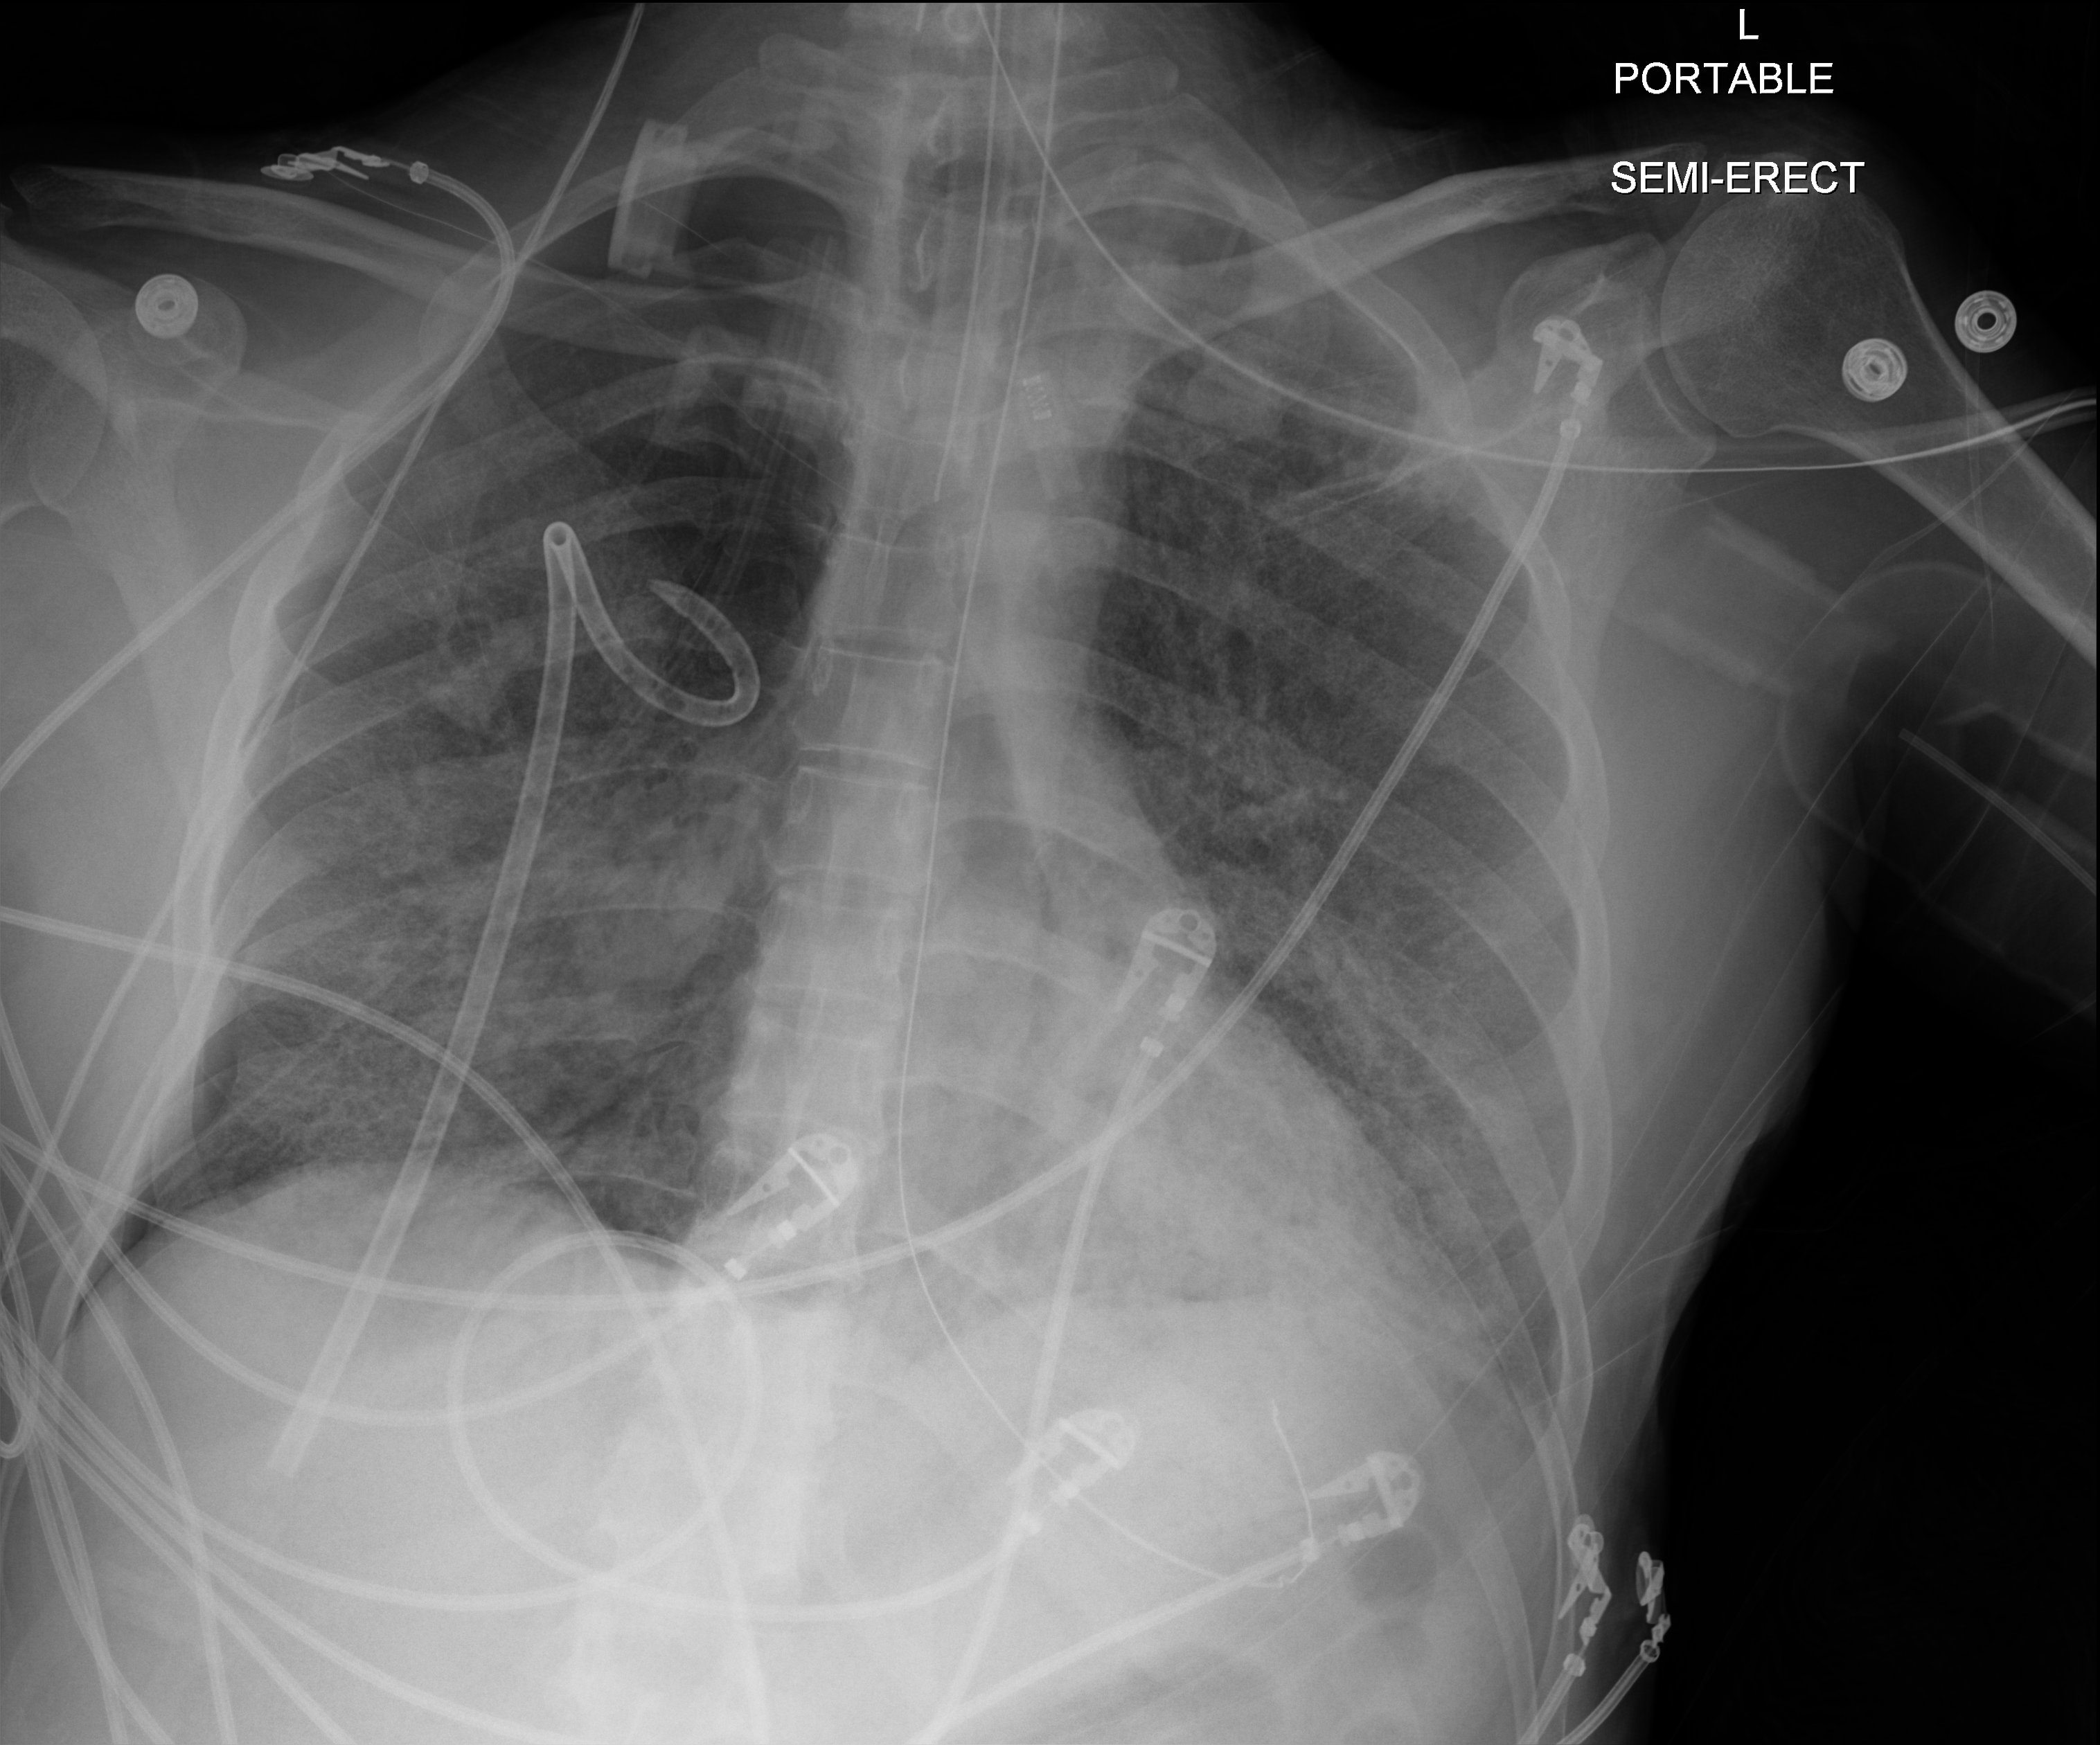
Chest radiograph, anteroposterior (AP) projection. Adult patient hospitalised with COVID-19, age 18–59 years.
Hospital-stay facts (about this admission, not read from this image; timing relative to this image not recorded):
- mechanically ventilated during this hospital stay: yes